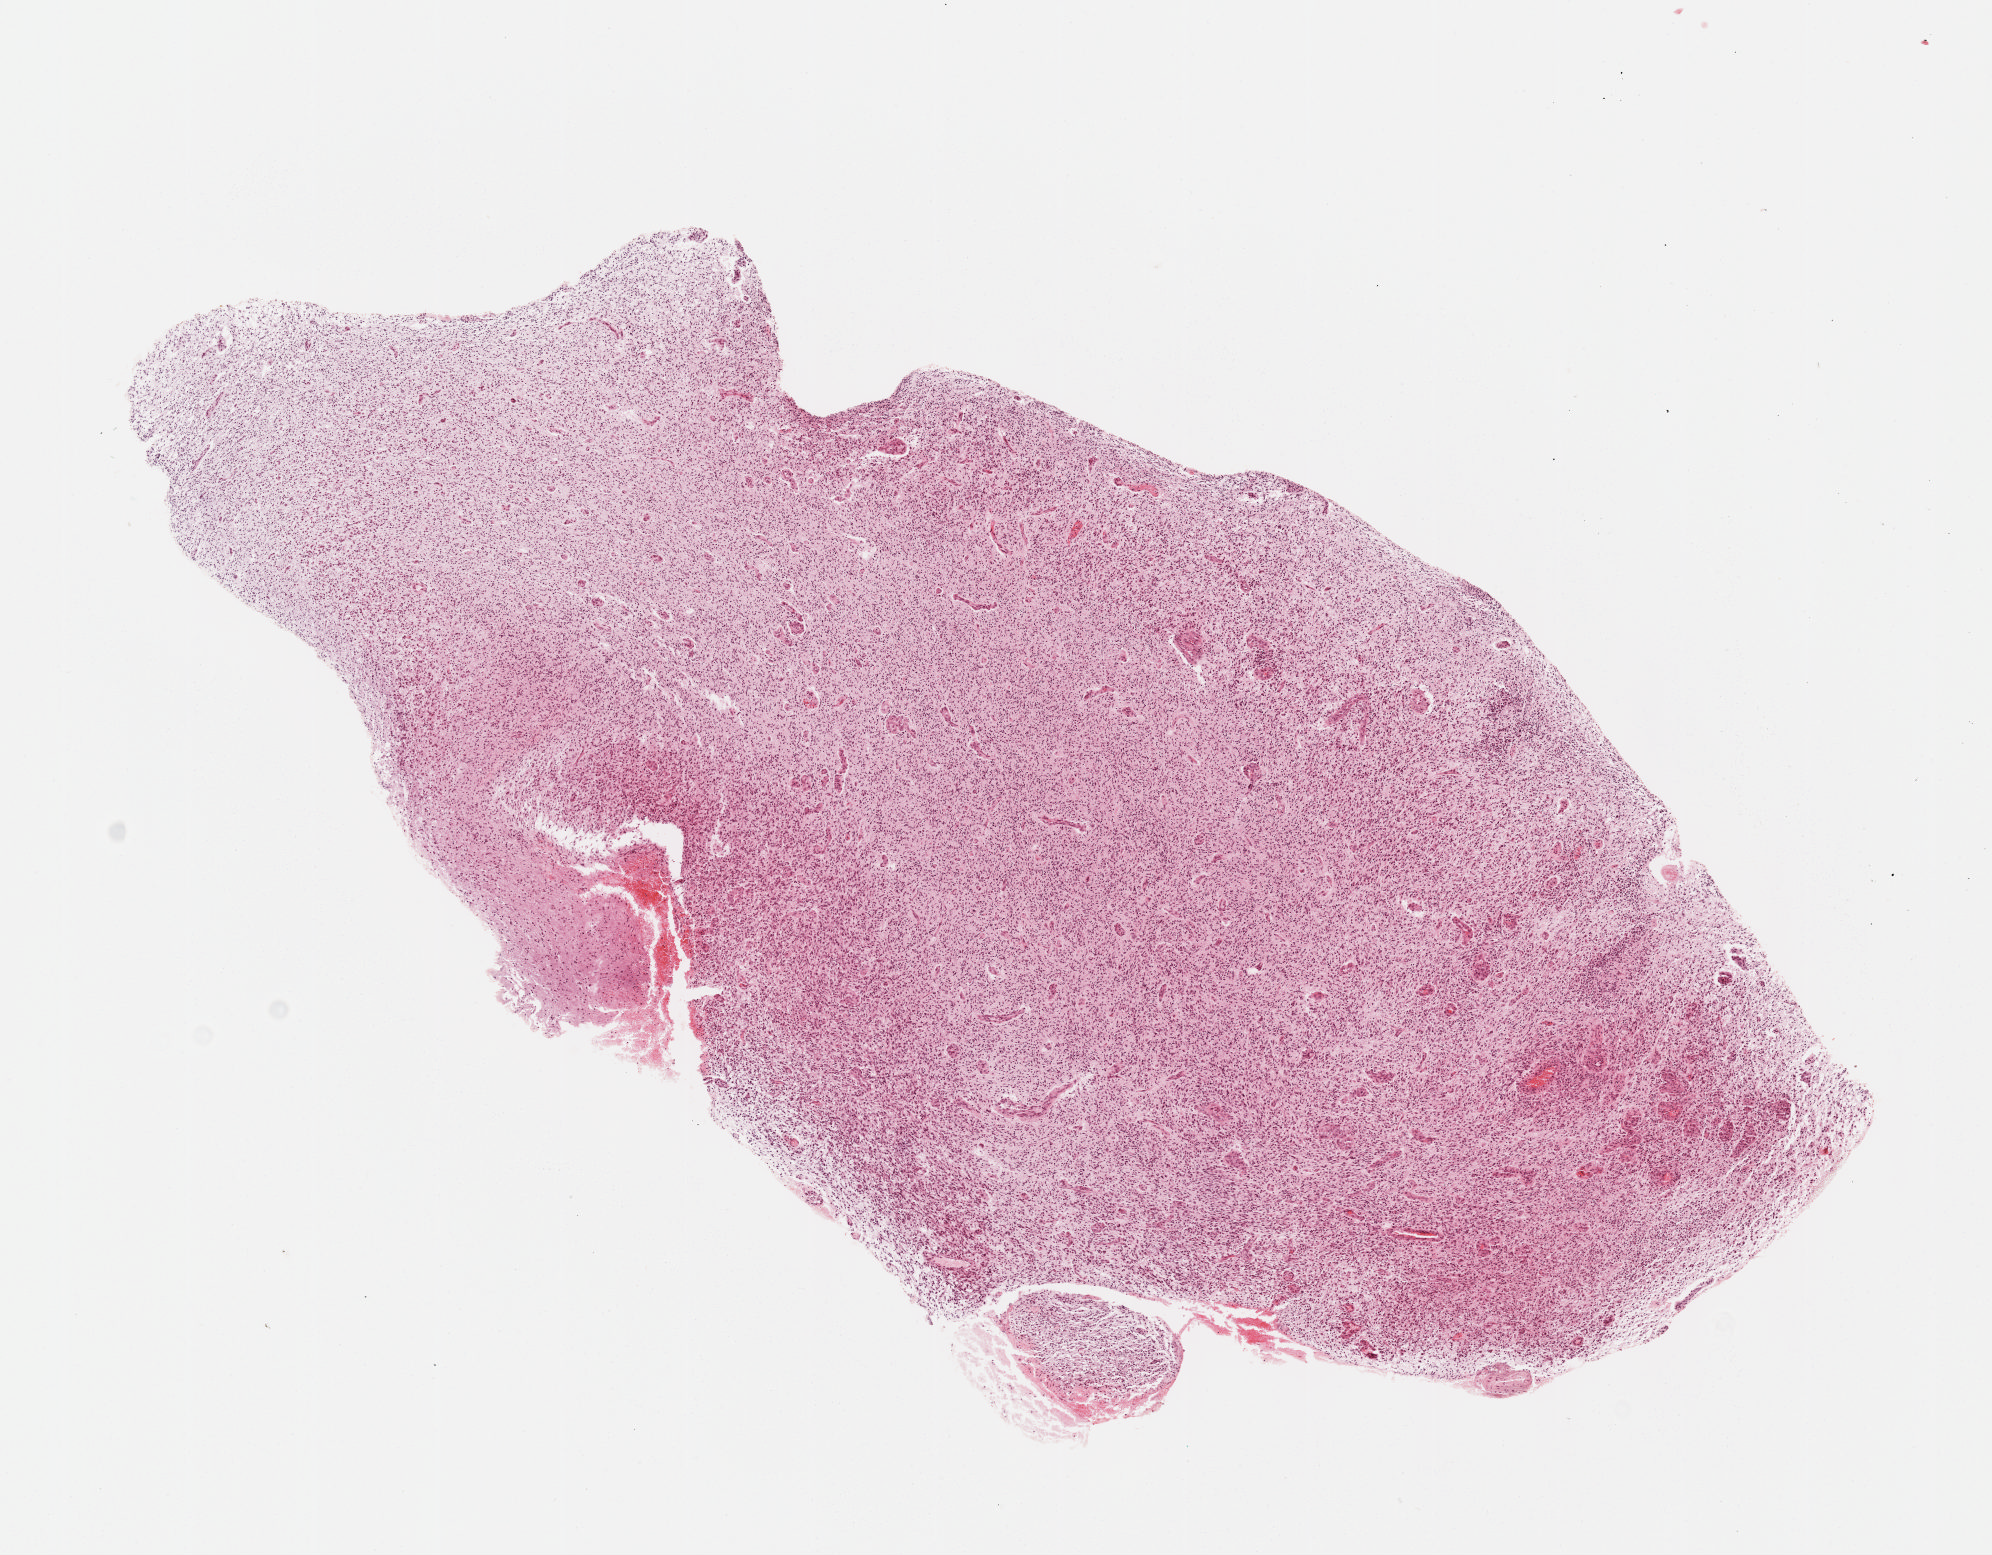
Digitized Hematoxylin and eosin (H&E) stained tissue section (whole slide) — shown as a low-resolution overview of the whole scanned area (about 8.0 x 6.3 mm); formalin-fixed paraffin-embedded (FFPE) diagnostic section; brain, primary tumour sample. Male patient; age at initial diagnosis 62 years.
• diagnosis: Glioblastoma